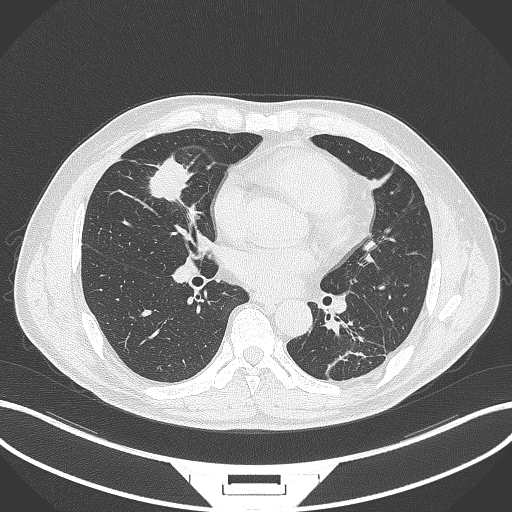
Chest CT, one axial slice. Position 138 of 399 along the scan axis. 120 kVp. Lung window (W 1500 / L -600 HU). 1 mm slice thickness. 512 × 512 image matrix, field of view 400 × 400 mm. Male patient, age 59 years. Case-level facts recorded for this patient, not image findings: clinical TNM (as recorded): T2a N1 M0.
Structures marked on this image (bounding box drawn by a radiologist):
- lung tumour (recorded histology: adenocarcinoma): bounding box [x1, y1, x2, y2] px = [145, 150, 194, 207]